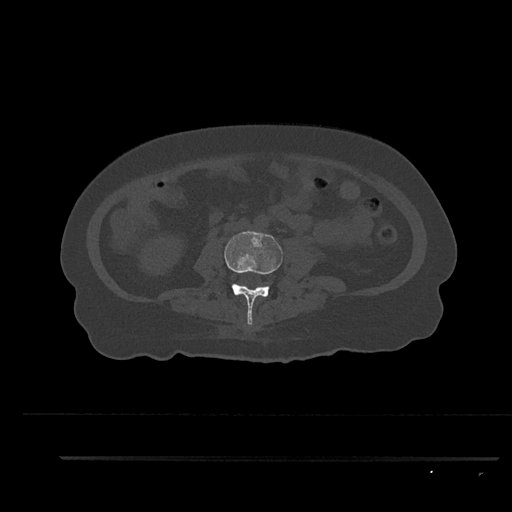
CT including the spine, one axial slice; position 75 of 797 along the scan axis; reconstruction kernel Br40s/3; 120 kVp; bone window (W 1800 / L 400 HU); 512 × 512 image matrix. Patient: female, 44 years. From the clinical record (not read from this slice): primary cancer: renal.
Structures marked on this image (semi-automatically segmented with operator editing):
- L3 vertebra: bounding box (x1, y1, x2, y2) in pixels: (224, 231, 283, 325)